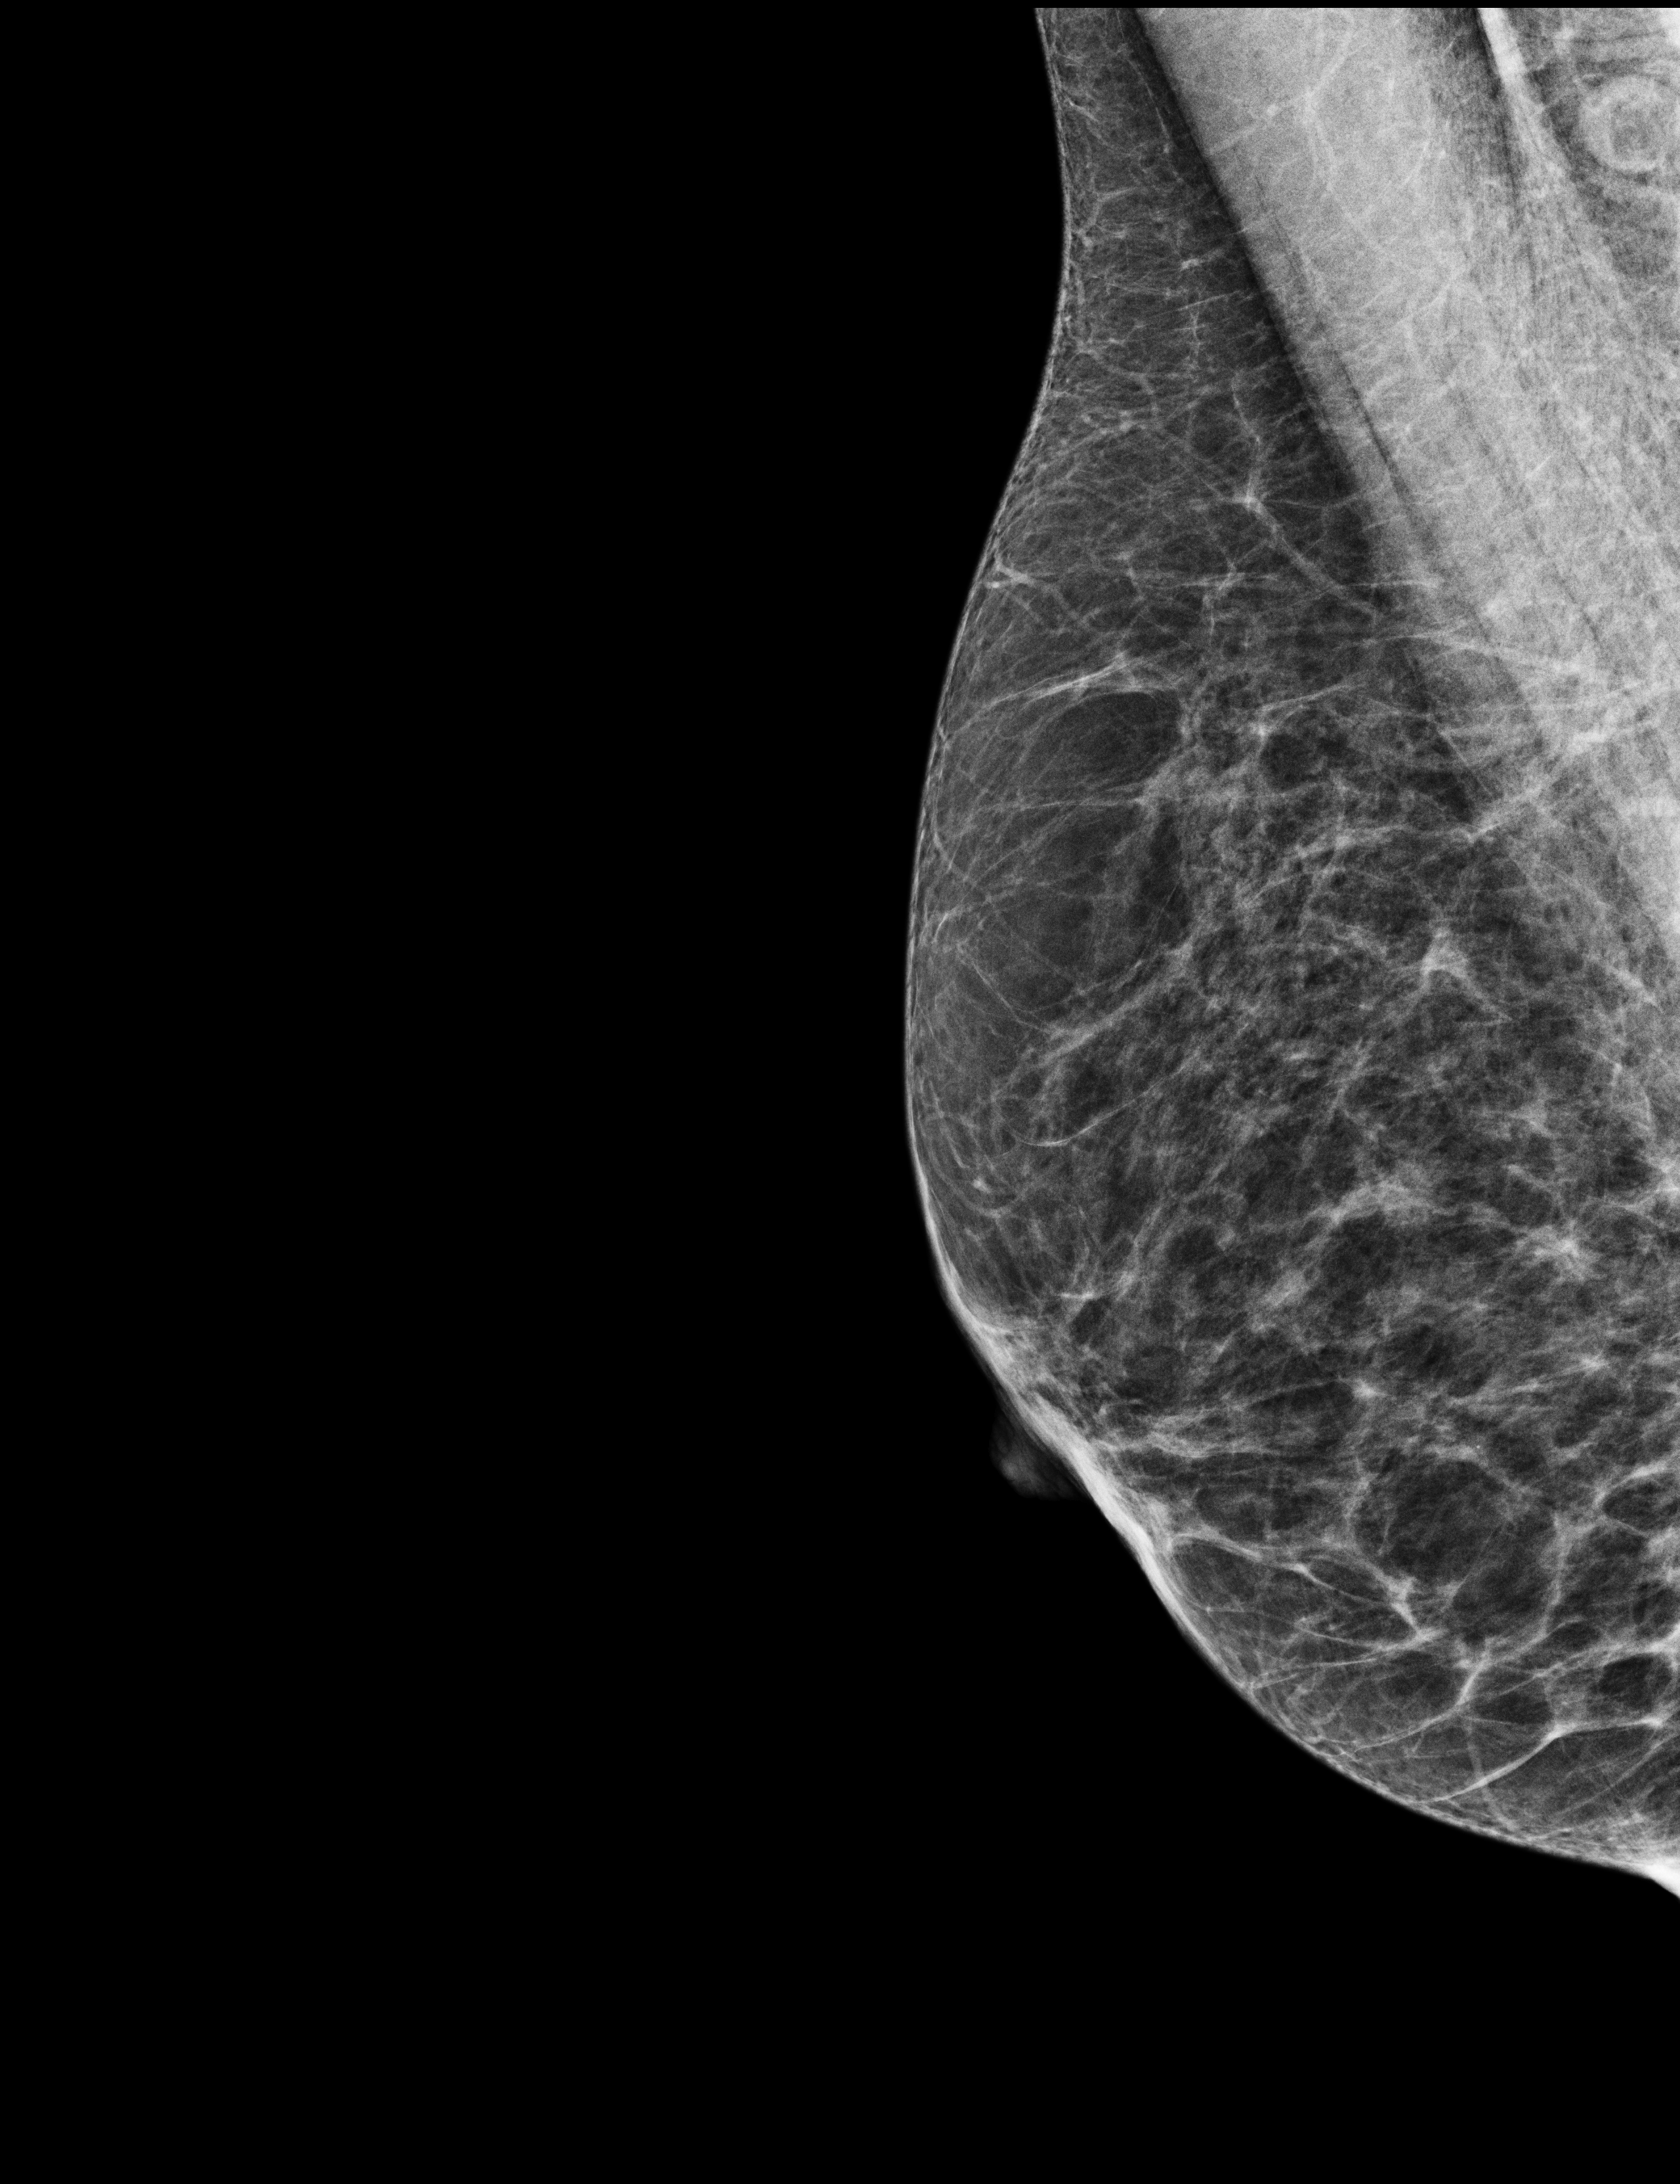
Annual screening mammography examination. Patient aged 64 years (female).
Image type: full-field digital mammogram. Breast: right. Projection: MLO view. BI-RADS breast density category at the screening exam (both breasts, scale 1–4): 3. Final BI-RADS category for the screening round (tomosynthesis exam, both breasts): category 1. Recall: no recall after this screen.